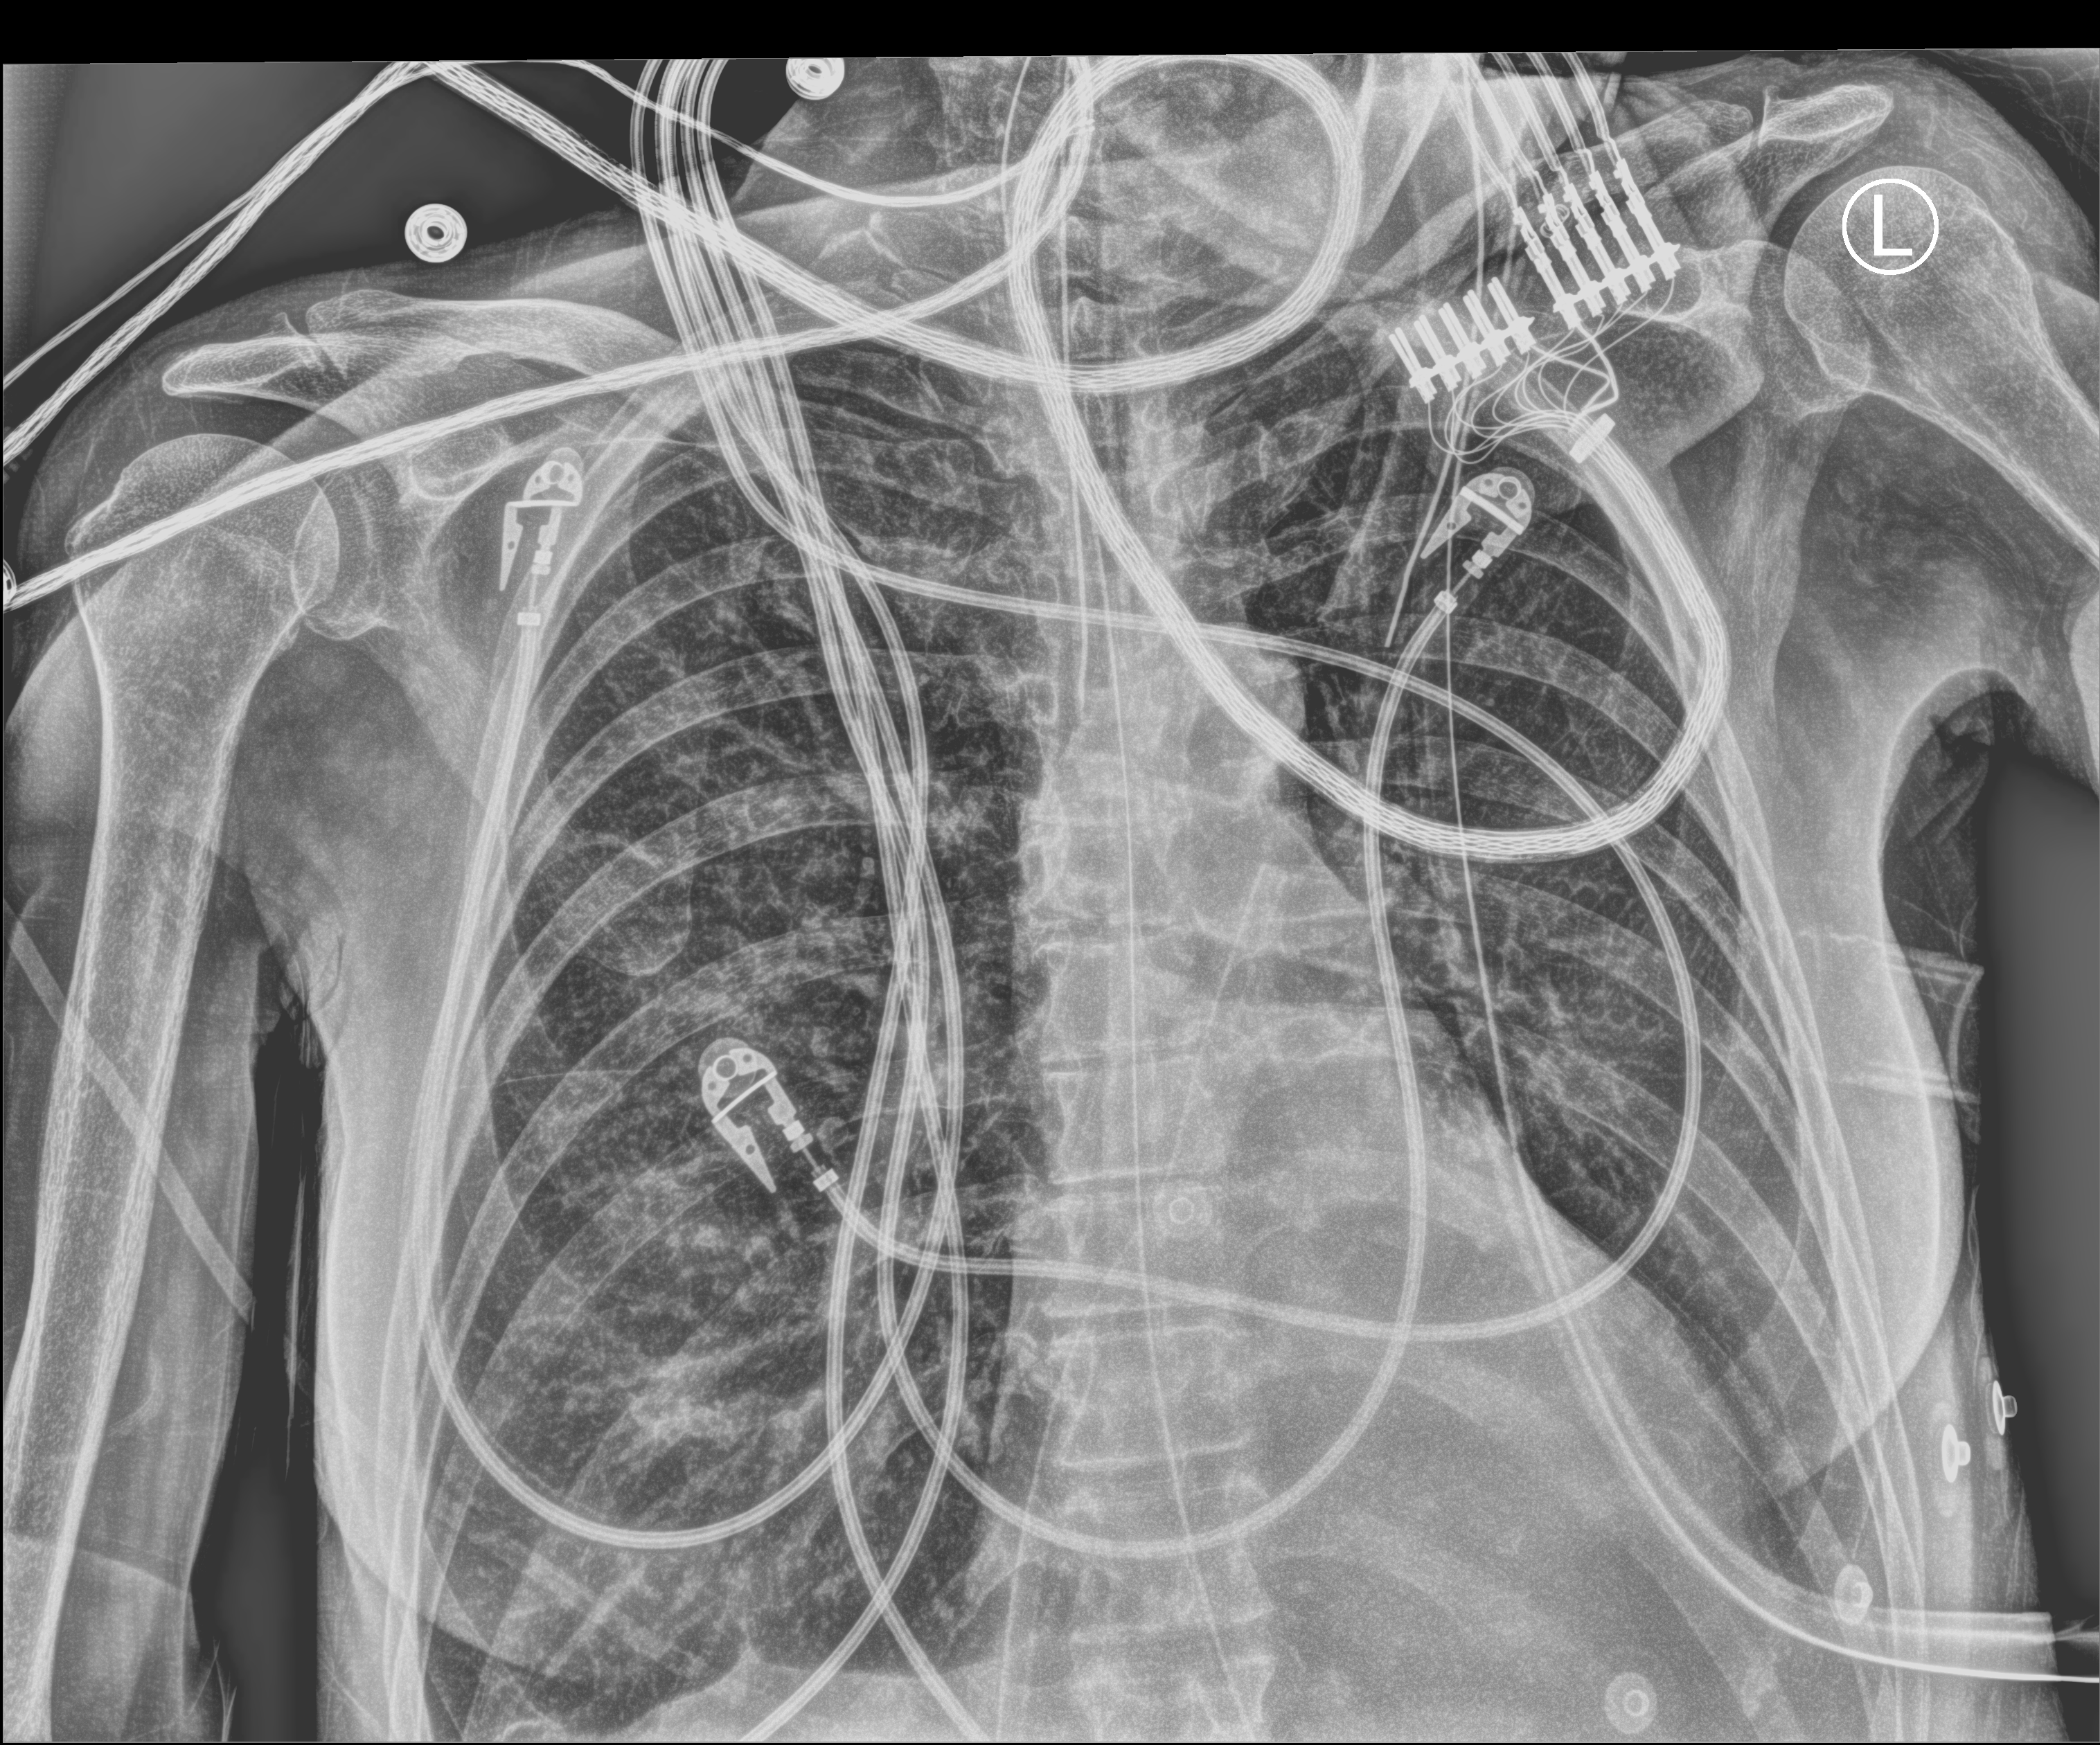
Portable chest radiograph; anteroposterior (AP) projection. Patient hospitalised with COVID-19; female, aged 60–74 years.
Hospital-stay facts (about this admission, not read from this image; timing relative to this image not recorded):
- mechanically ventilated during this hospital stay: yes
- admitted to intensive care during this hospital stay: yes